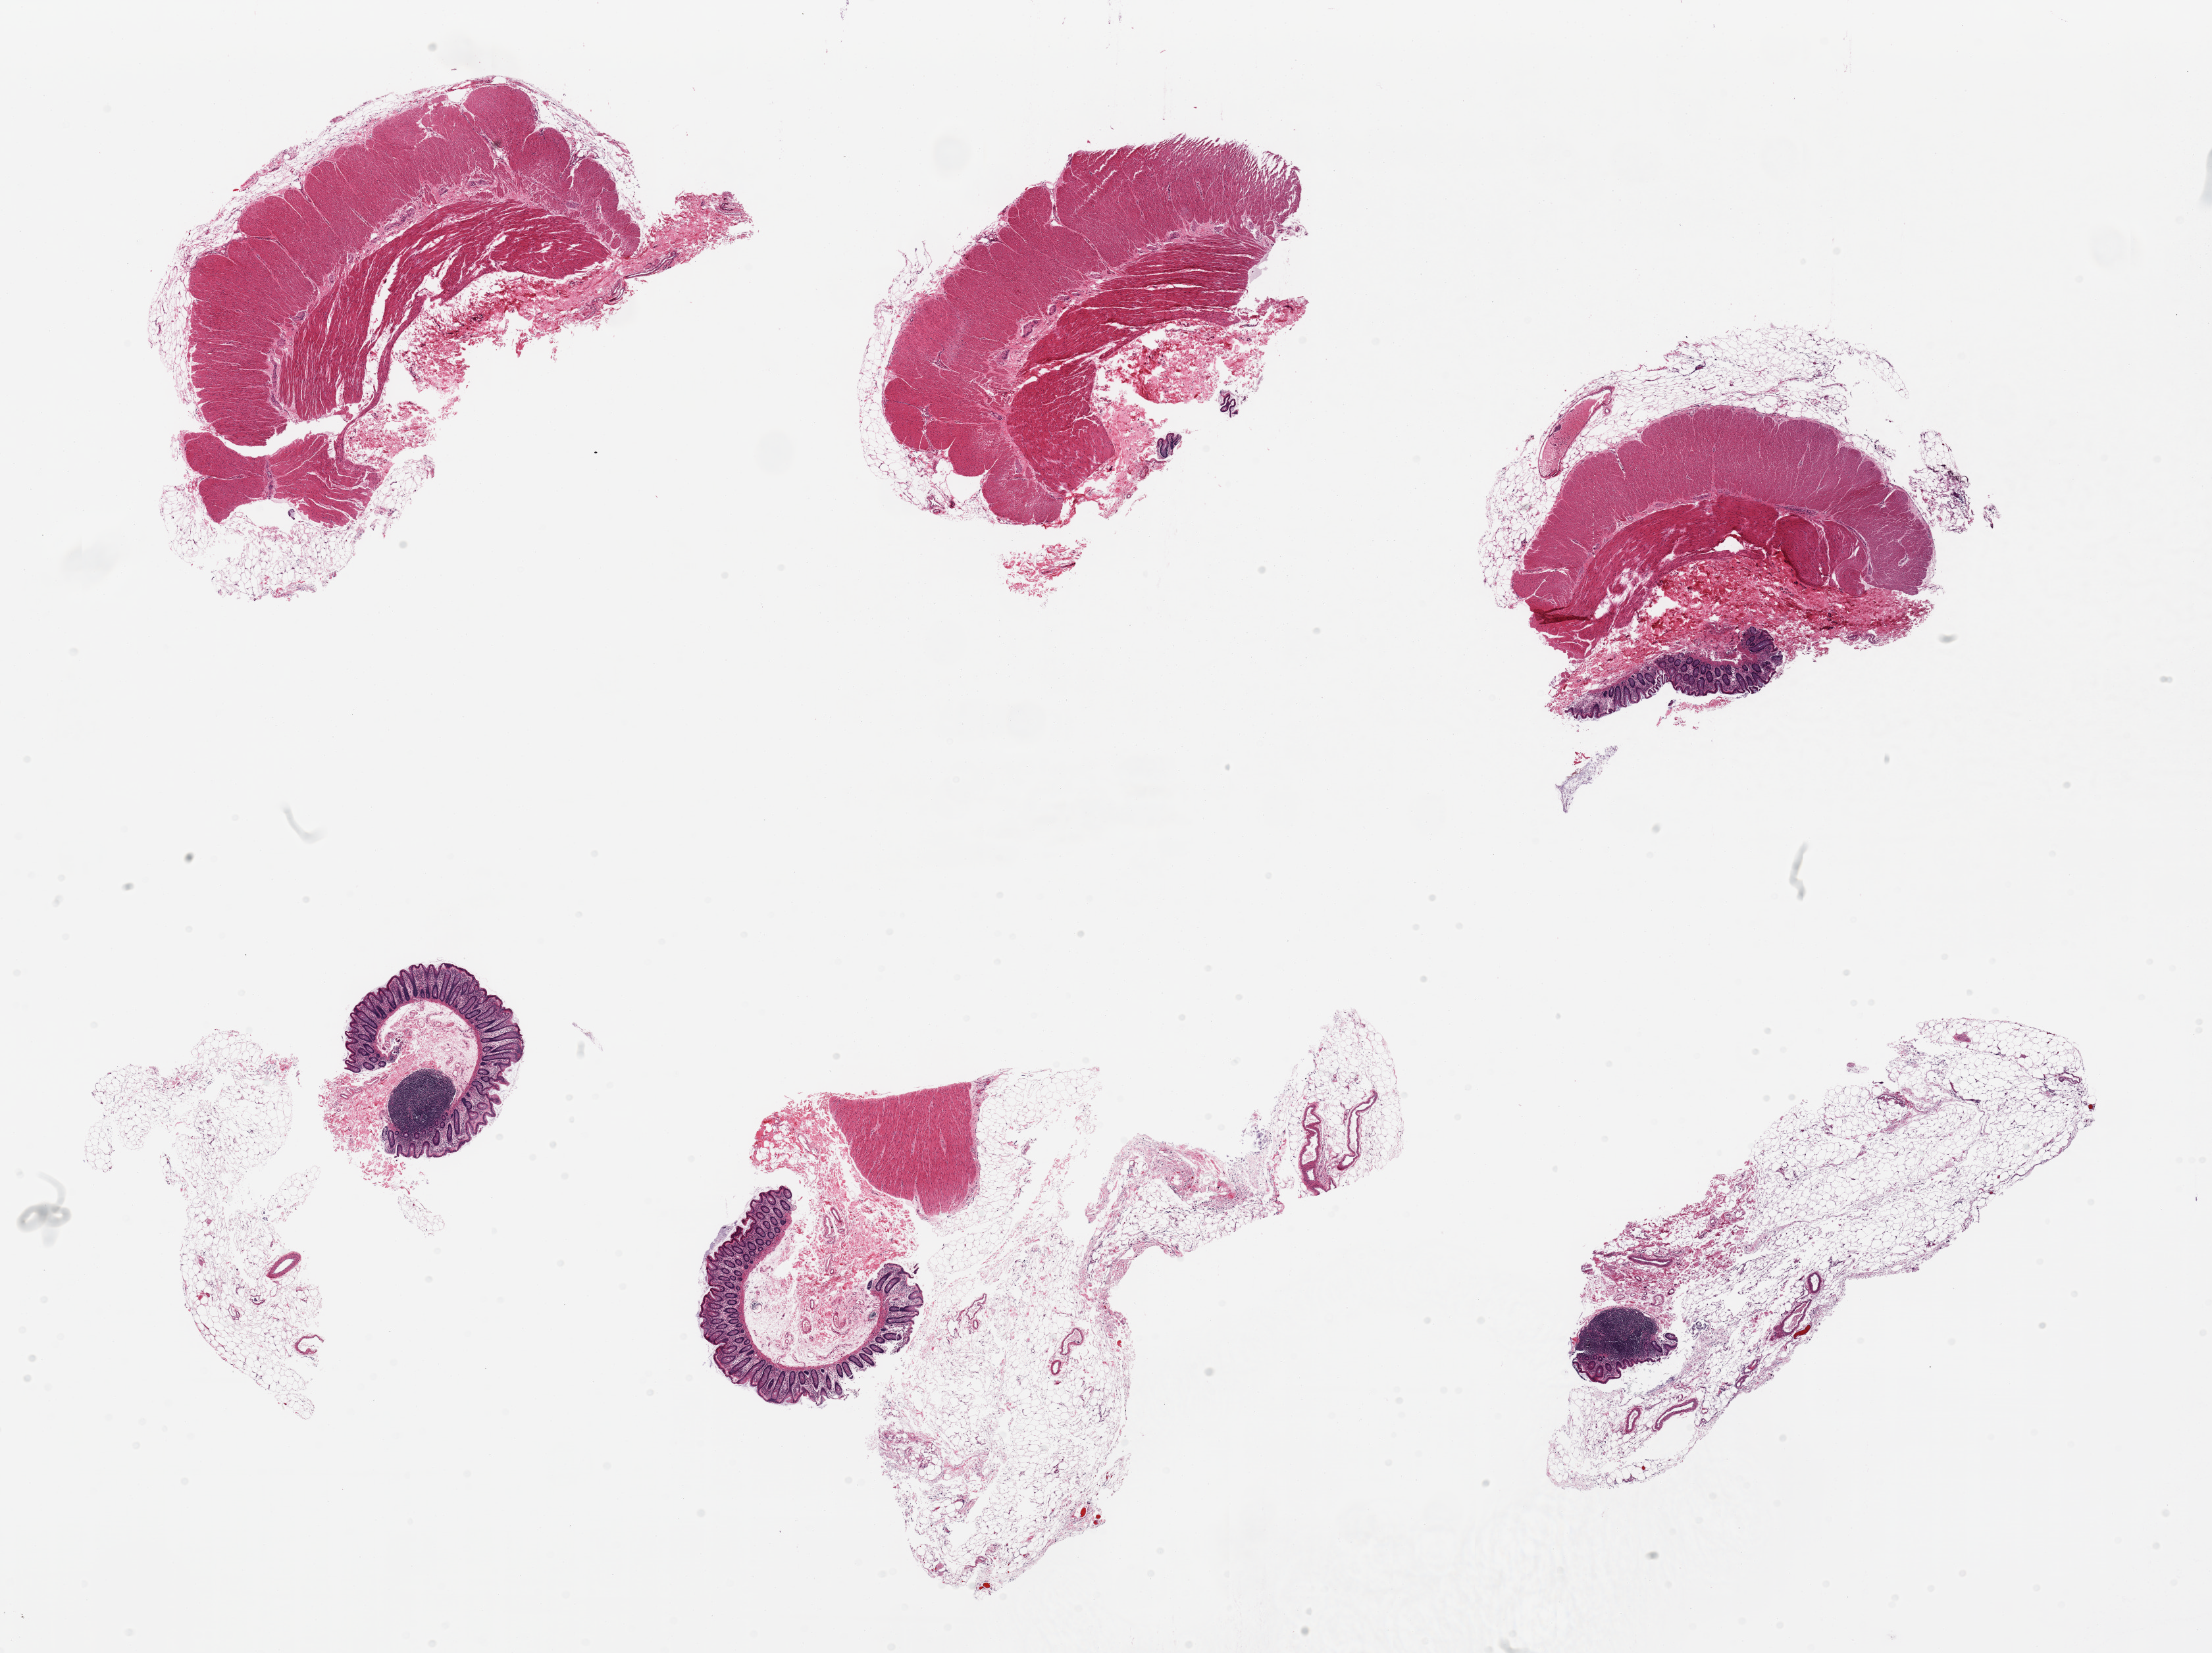
Whole-slide image, hematoxylin and eosin (H&E) stain, brightfield, shown as a low-resolution overview of the whole scanned area (about 26.6 x 19.9 mm, slide scanned at 20x). PAXgene-fixed paraffin-embedded (PFPE) section. Section of transverse colon (target tissue). Donor tissue sample. Donor: male.
- review note (as recorded): 6 pieces; 3 are predominantly muscularis, 3 are predominantly fat and mucosa